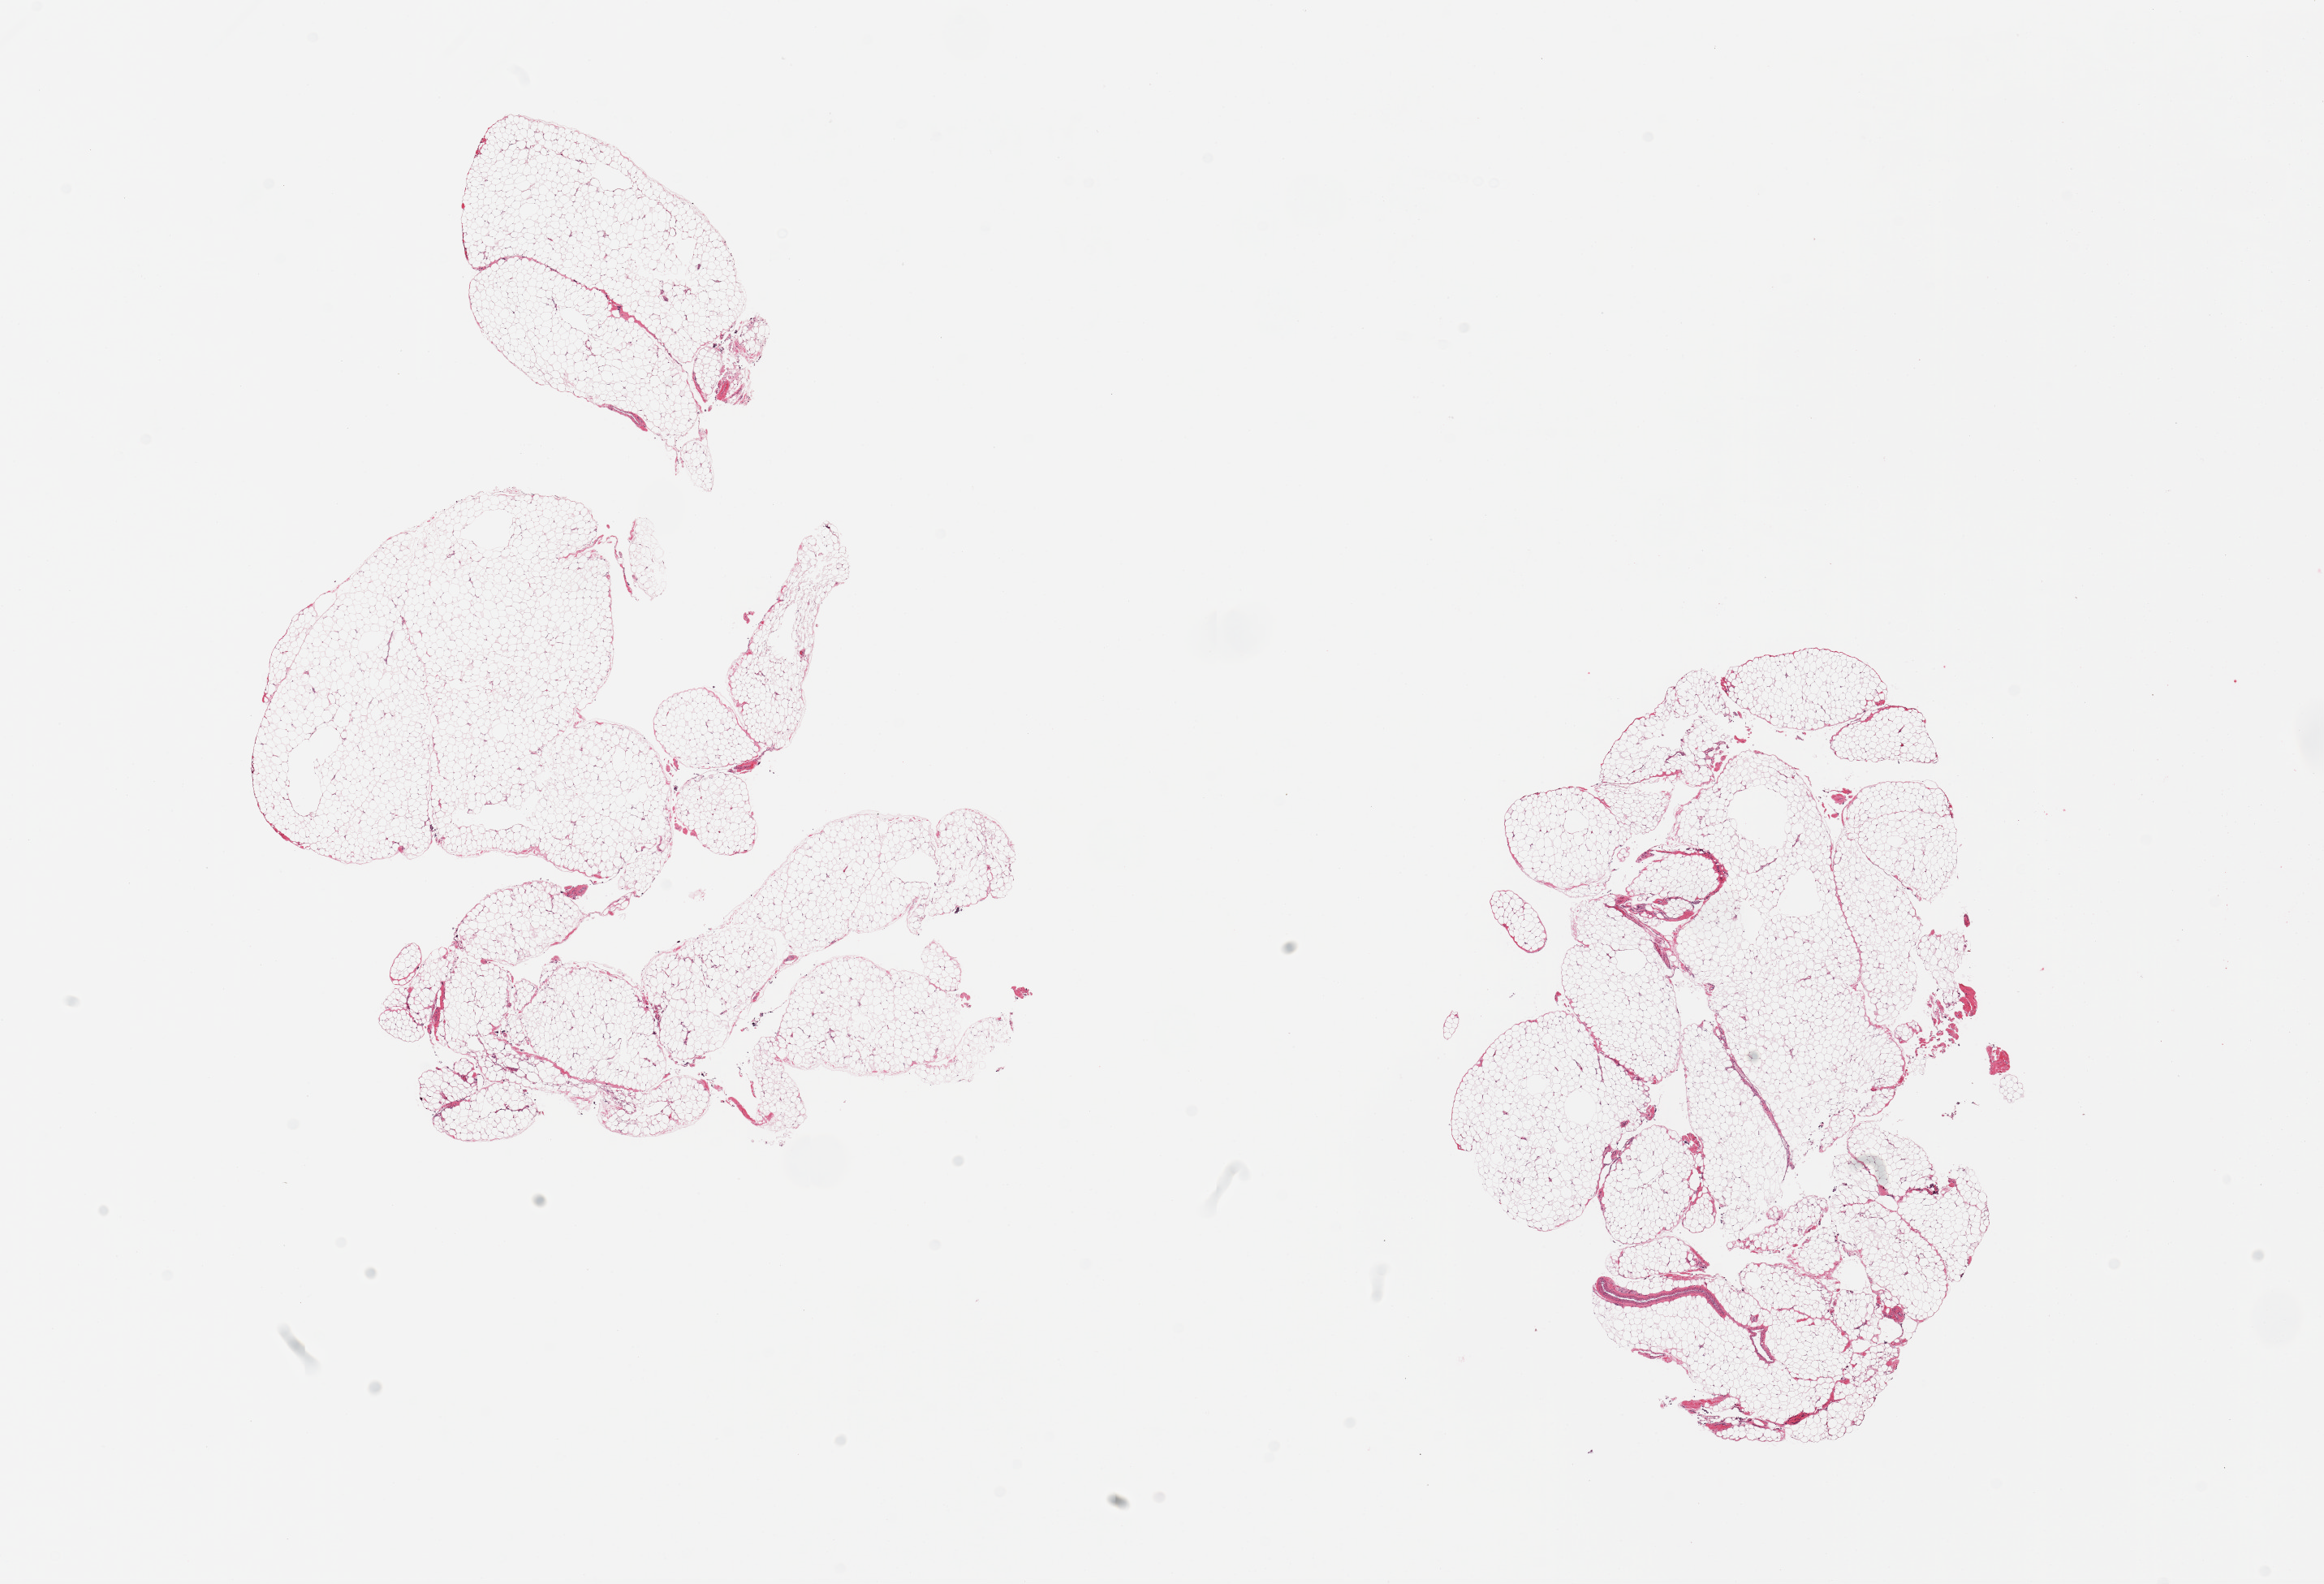
Digitized haematoxylin and eosin-stained section — a low-resolution overview of the entire scanned area, about 22.6 x 15.4 mm (acquisition: 20x scan), PAXgene-fixed, paraffin-embedded tissue, target tissue: omentum, tissue donor sample.
Reviewer comment on this tissue sample: 2 pieces.